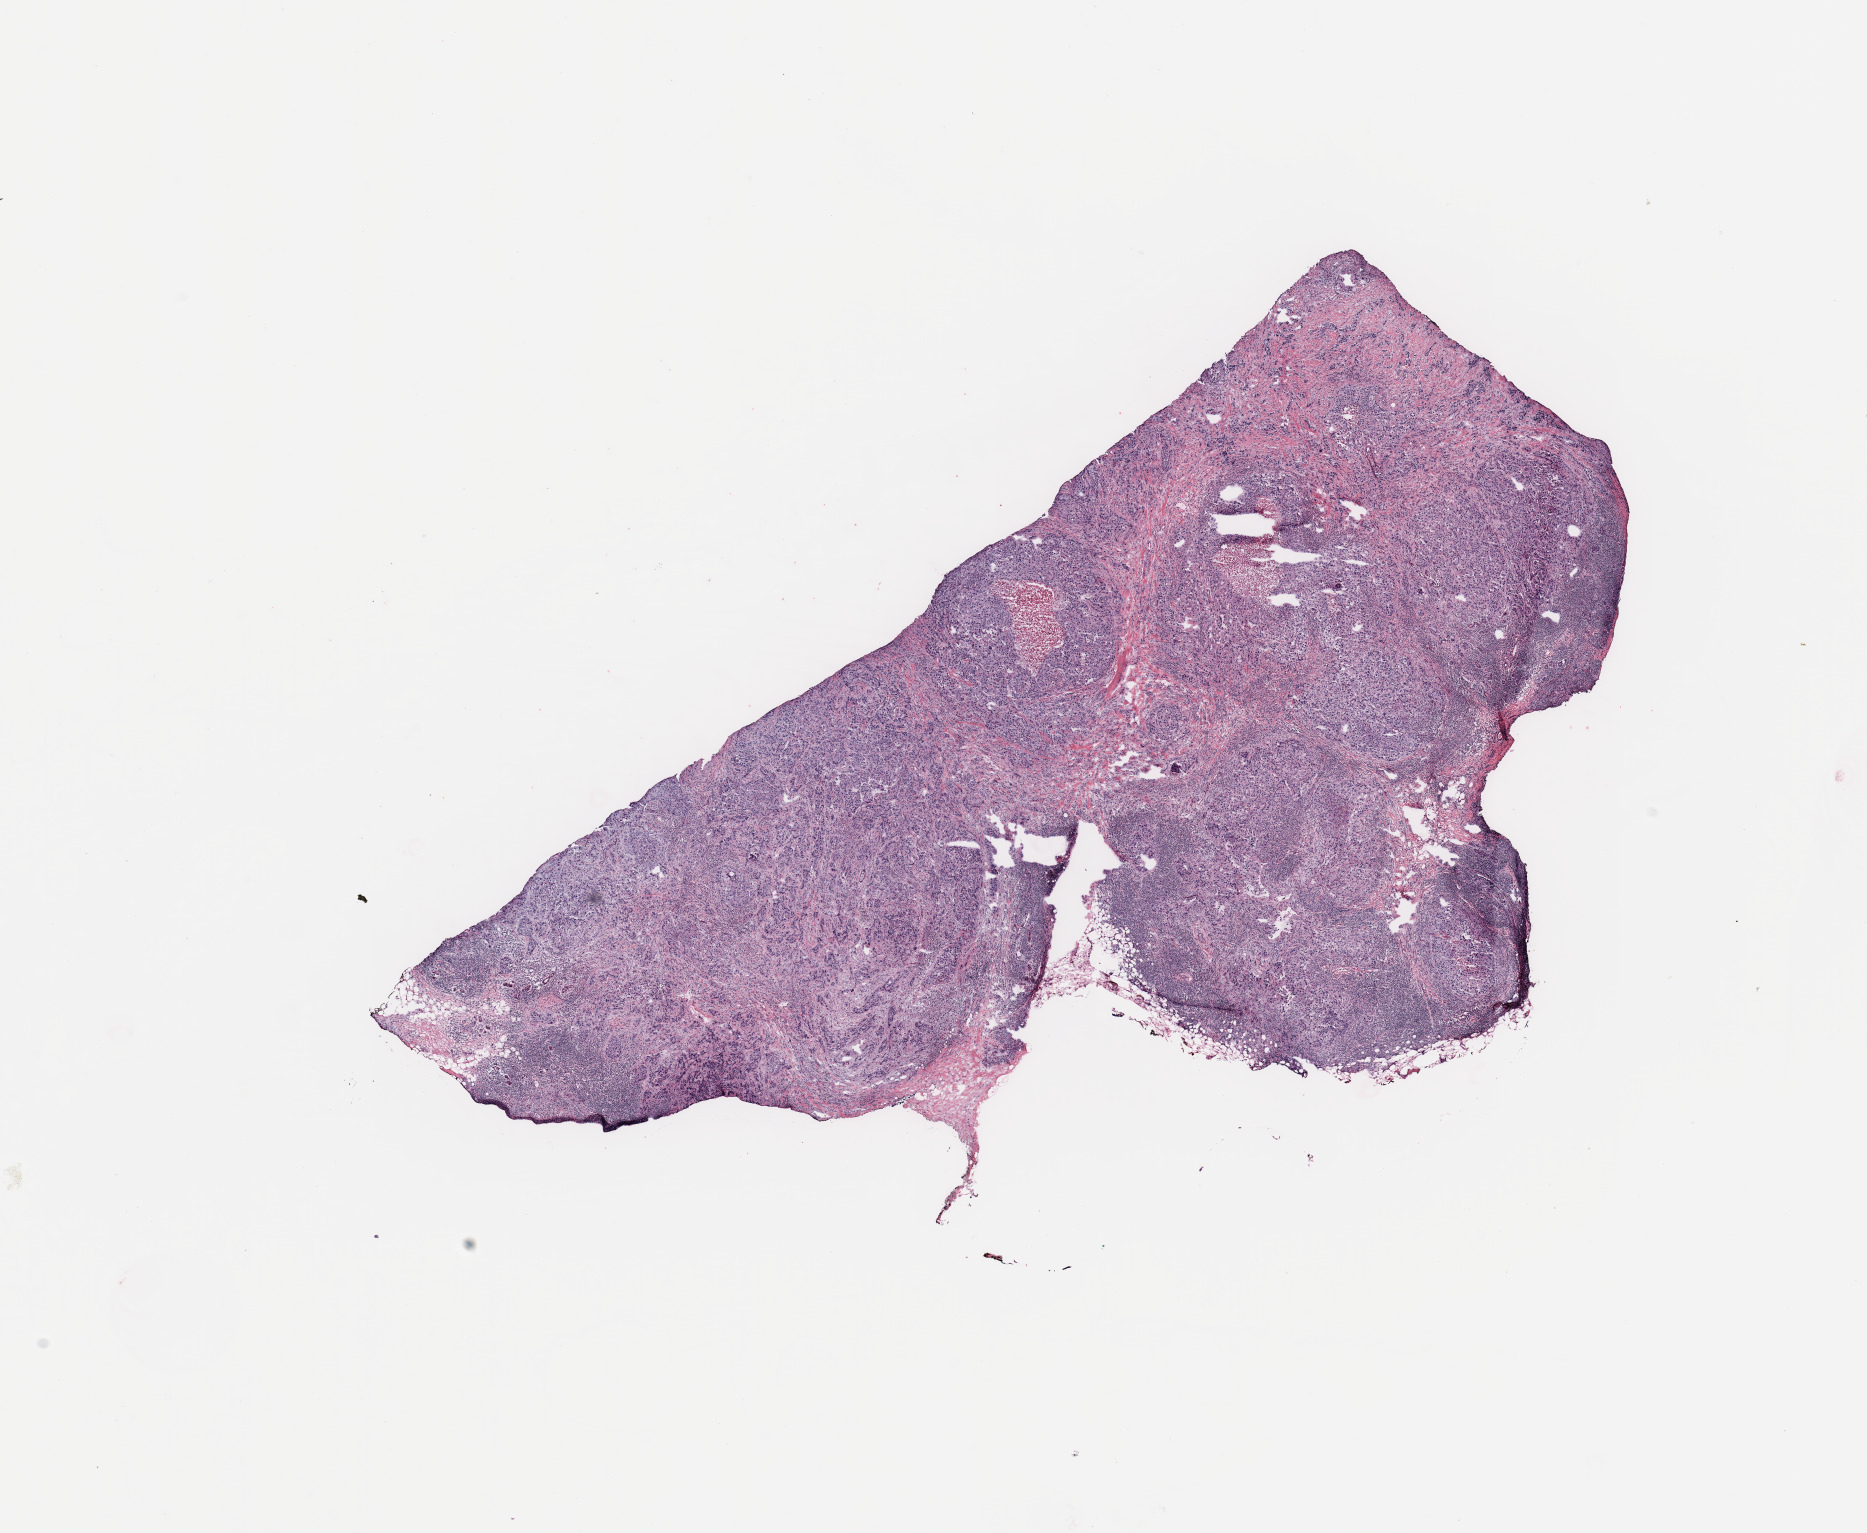
Hematoxylin and eosin (H&E) stained whole-slide image — a low-resolution overview of the entire scanned area, about 14.8 x 12.1 mm; breast, tissue type not recorded.
• patient diagnosis (cohort enrolment): breast cancer (breast)